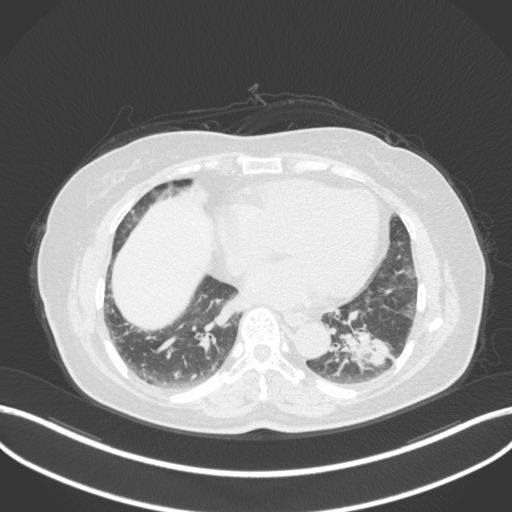
Chest CT, one axial slice. Slice 140 of 307 in the series (ordered by position). Reconstruction kernel B31f. 120 kVp. Lung window (W 1500 / L -600 HU). 1 mm slice thickness. 512 × 512 image matrix, field of view 400 × 400 mm. Female patient, age 59 years. From the clinical record (not read from this slice): clinical TNM (as recorded): T2a N0 M0; histopathological grade: G2-3.
Annotated regions visible in this slice (bounding box drawn by a radiologist):
- lung tumour (recorded histology: adenocarcinoma): bounding box (x1, y1, x2, y2) in pixels: (337, 323, 398, 381)